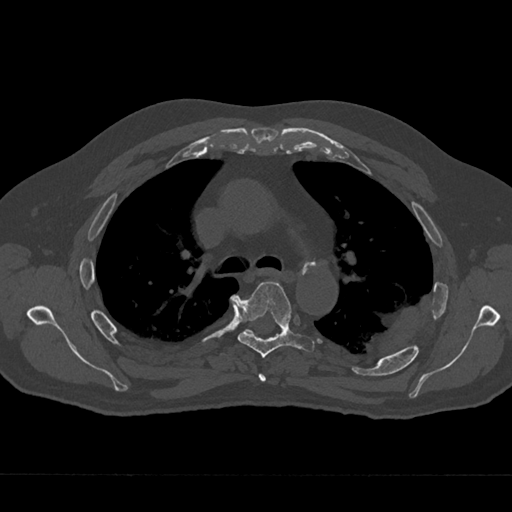
CT including the spine, one axial slice; slice 473 of 797 in the series (ordered by position); reconstruction kernel Br40s/3; bone window (W 1800 / L 400 HU); 0.5 mm slice thickness; 512 × 512 image matrix, field of view 377 × 377 mm. Male patient, age 75 years. Case-level facts recorded for this patient, not image findings: primary cancer: renal; vertebrae with lytic lesions (as recorded): T4.
Outlined on this slice (semi-automatic segmentation, software-assisted and operator-edited):
- T4 vertebra: bounding box <258,373,266,382> (left, top, right, bottom; pixels)
- T5 vertebra: <236,281,315,358>
- T6 vertebra: <246,329,253,334>